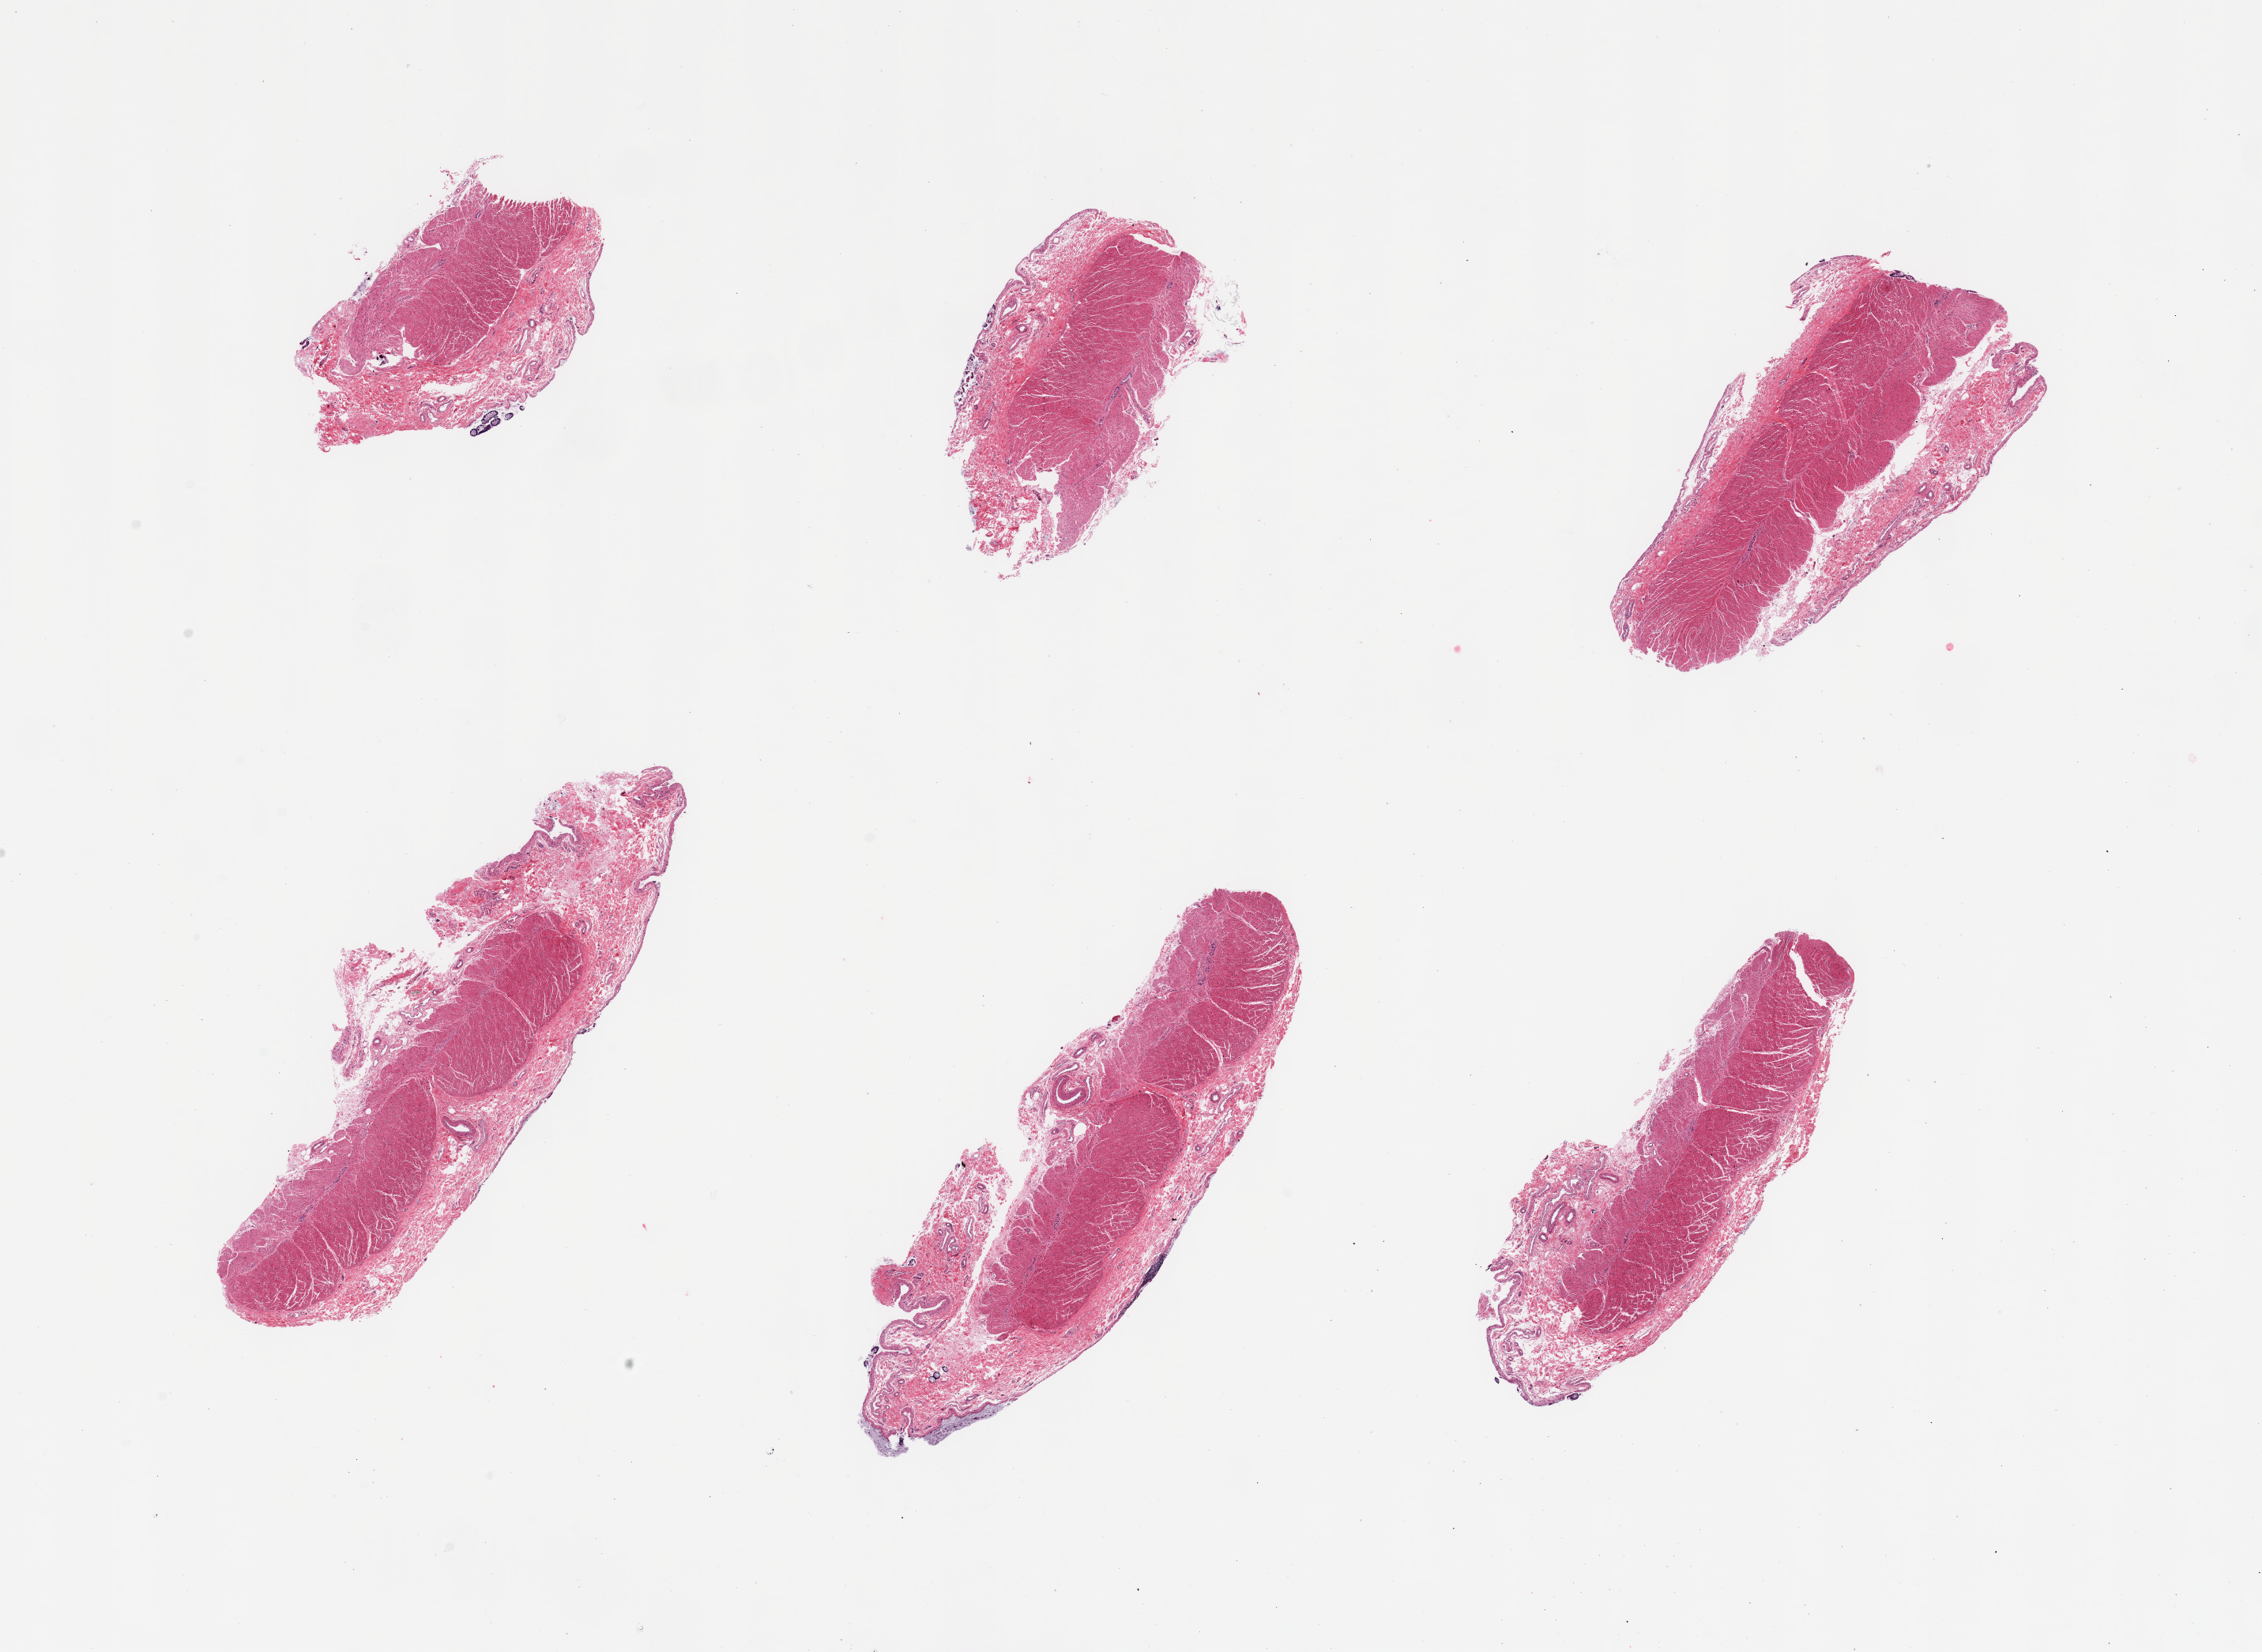
Hematoxylin and eosin (H&E) whole-slide image, whole scanned area (about 22.6 x 16.5 mm) shown as a low-resolution overview; PAXgene-fixed paraffin-embedded (PFPE) section; target tissue: sigmoid colon; tissue donor sample. Donor: female.
* reviewer comment on this tissue sample: 6 pieces, confirmed target muscularis